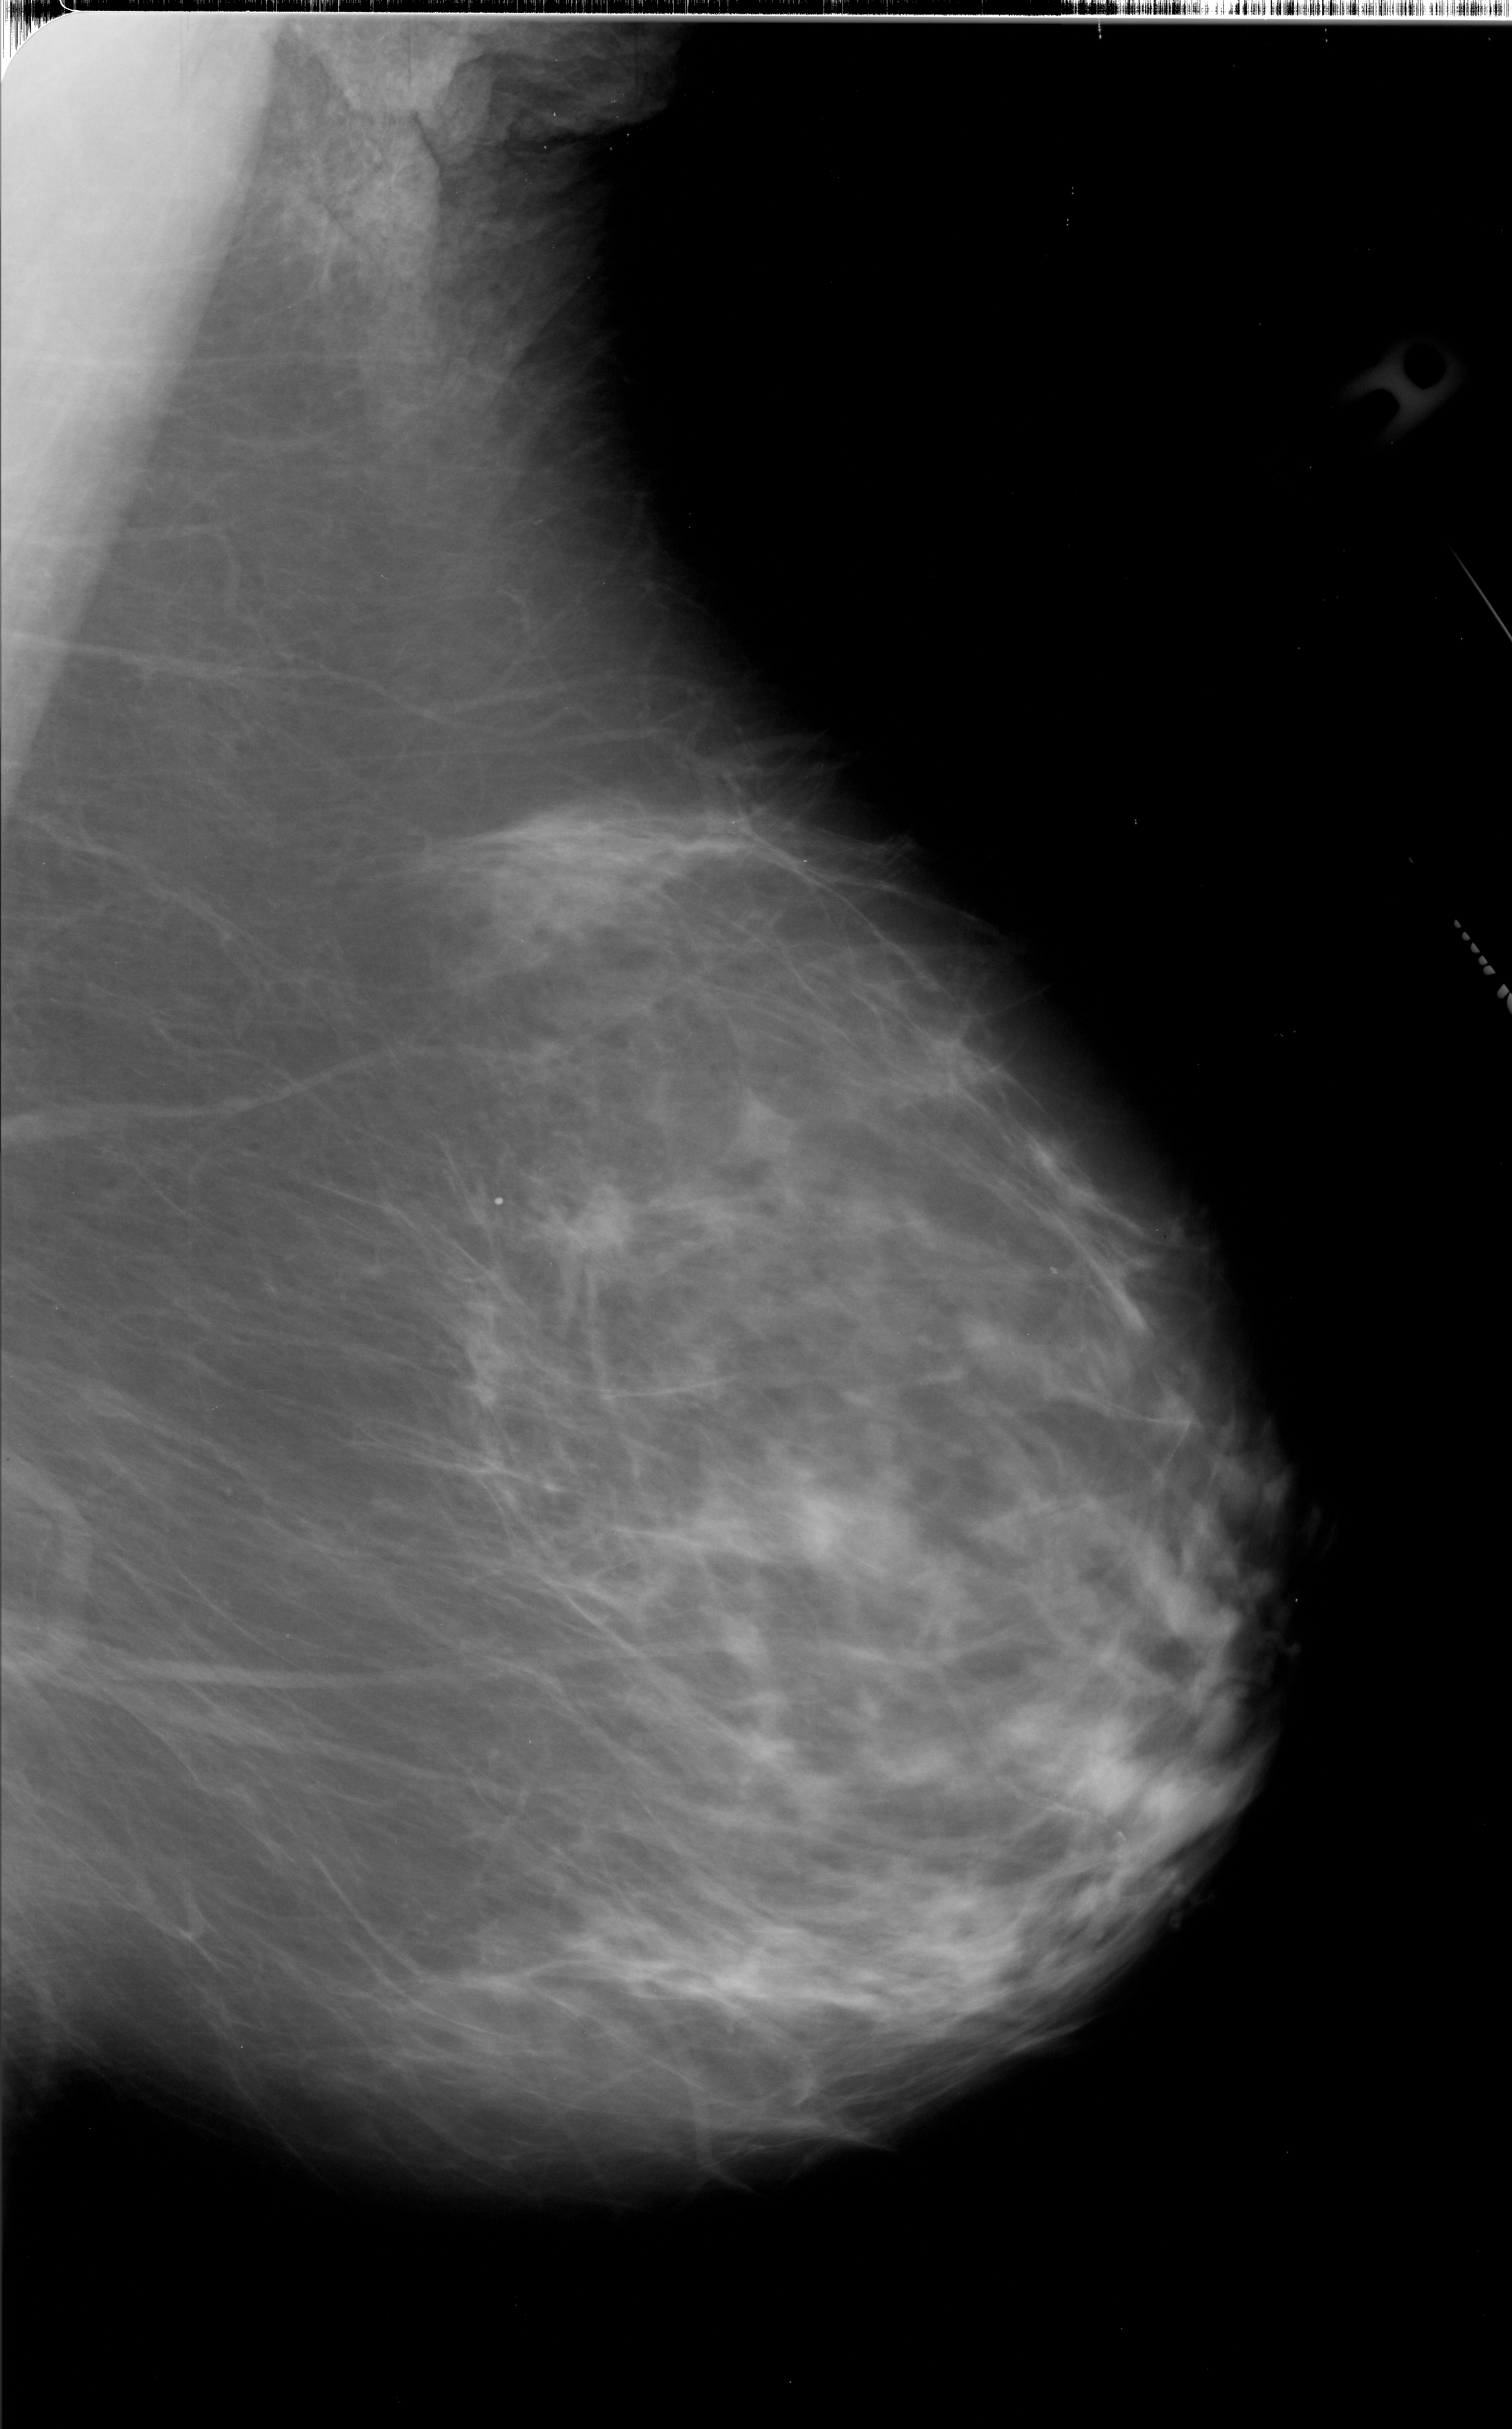
Scanned film-screen mammogram, right breast, mediolateral oblique (MLO) view, BI-RADS breast density category 2 (scale 1–4).
- Marked findings (only marked abnormalities are described; nothing is implied about the rest of the image): mass, shape irregular, margins spiculated; BI-RADS assessment category 5; pathology result (as recorded, not read from the image): malignant.